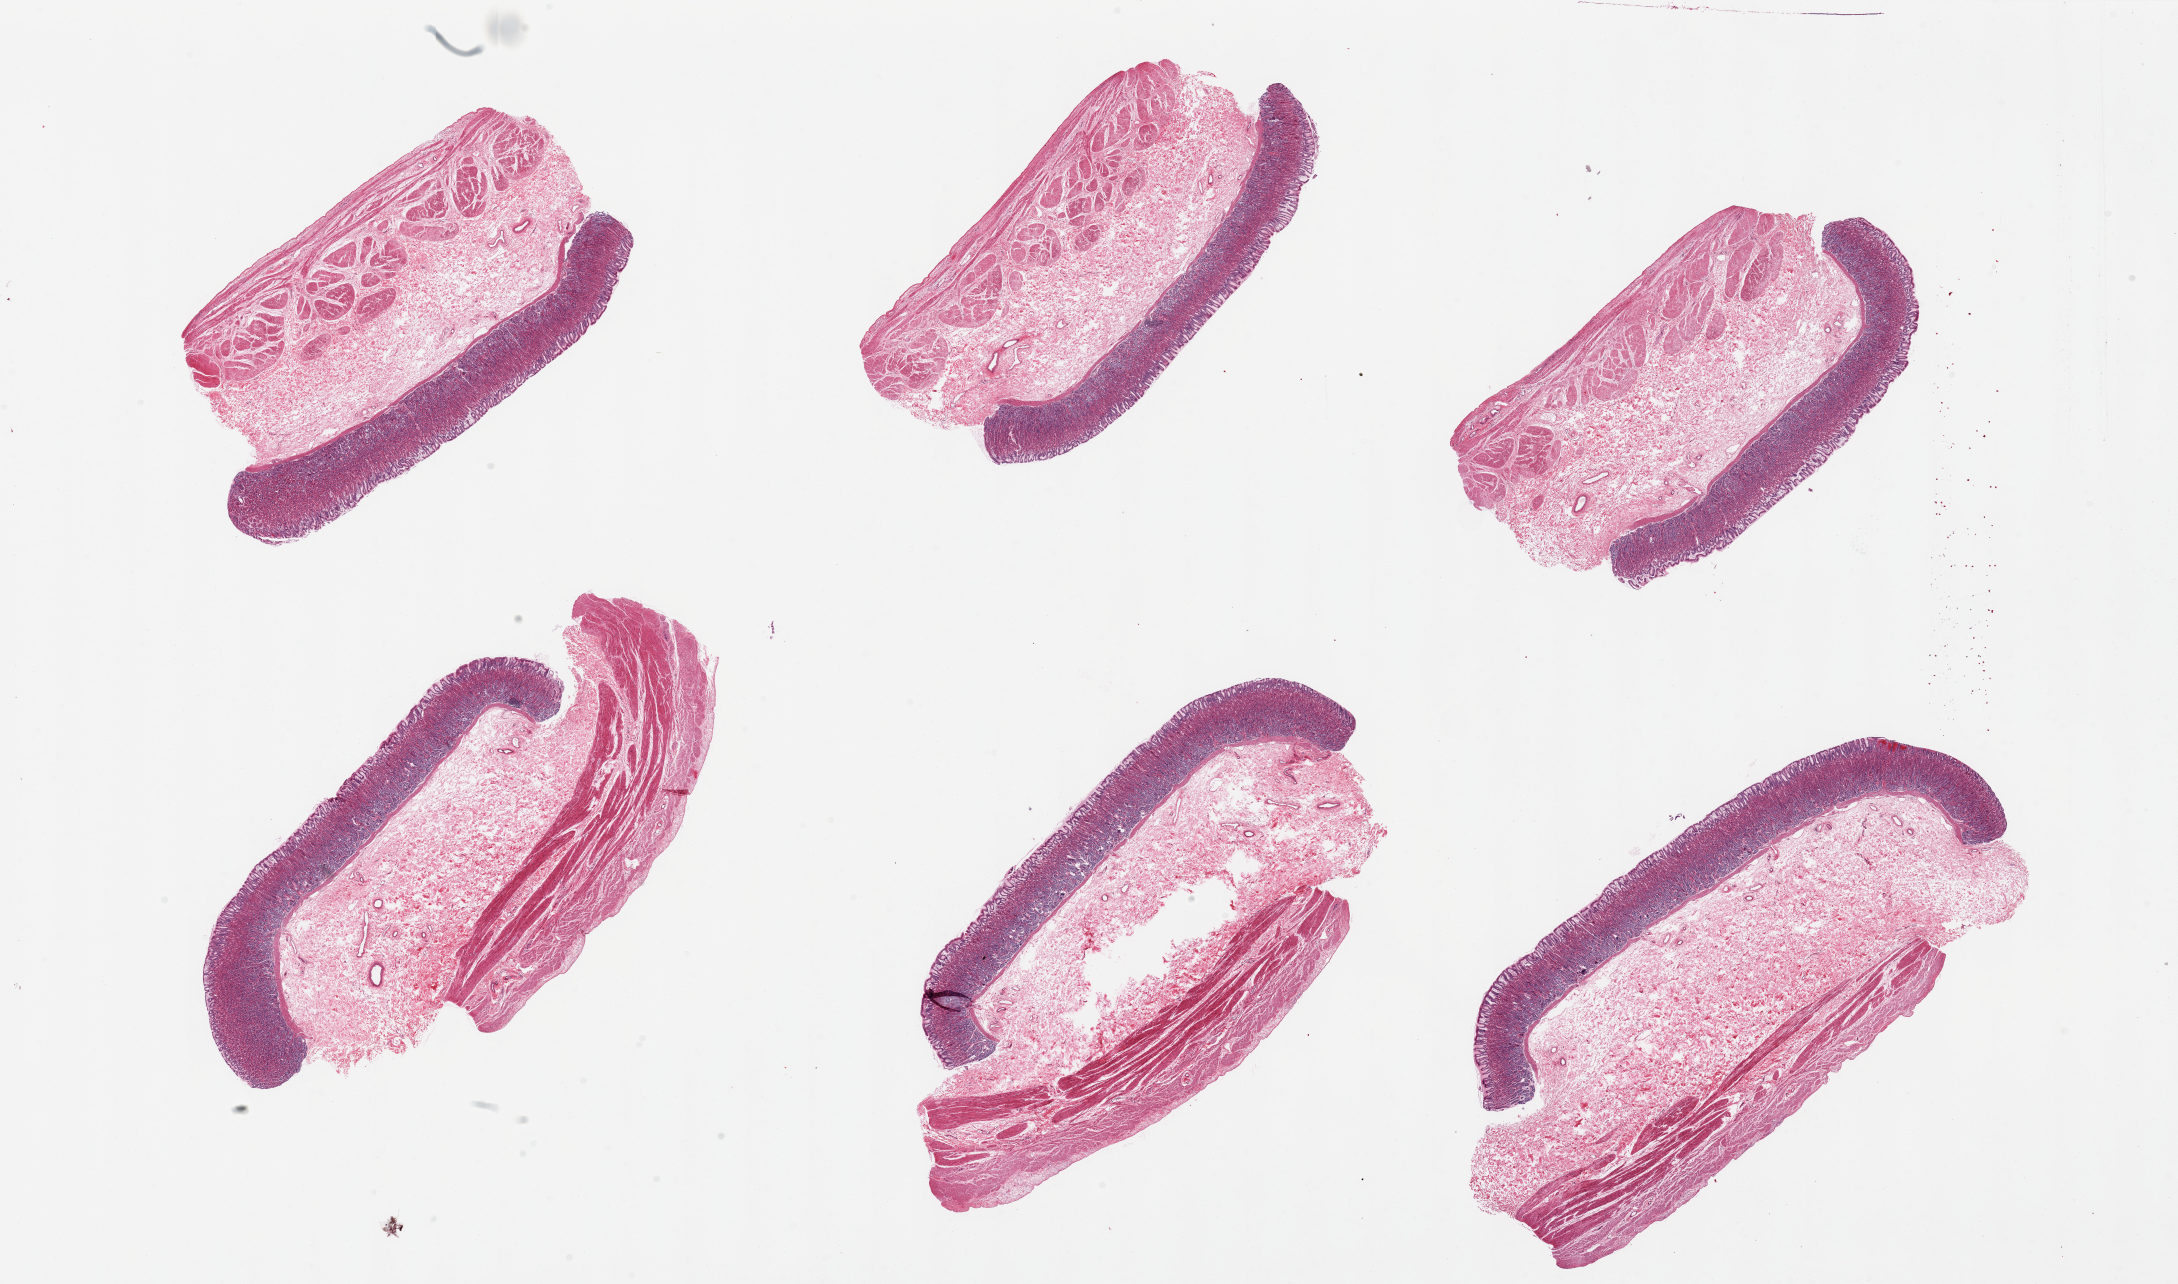
Whole-slide image, hematoxylin and eosin (H&E) stain, low-resolution overview of the scanned area, about 34.5 x 20.3 mm, PAXgene-fixed paraffin-embedded (PFPE) section, section of stomach (target tissue), donor tissue sample.
Review note (as recorded): 6 pieces; submucosal edema, full thickness.